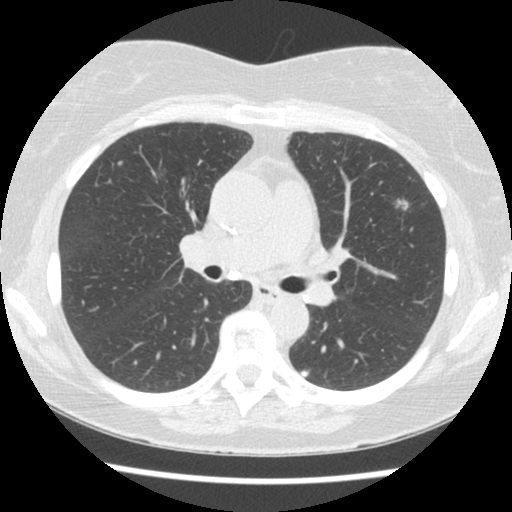
Low-dose screening chest CT, one axial slice. Slice 70 of 120 in the series (ordered by position). Reconstruction kernel STANDARD. 120 kVp. Lung window (W 1500 / L -600 HU). 2.5 mm slice thickness. 512 × 512 image matrix, field of view 310 × 310 mm.
Outlined on this slice (manually delineated by an expert):
- lesion 1 (tumor, upper lobe of left lung): bounding box <396,199,409,210> (left, top, right, bottom; pixels)